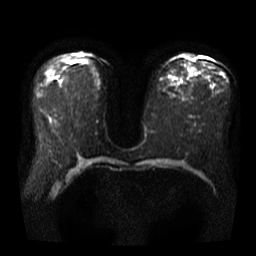
Breast MRI, one axial slice. Position 21 of 40 along the scan axis. Diffusion-weighted series; image 2 of 4 stored at this slice position (different b-values; order by instance number). 3 T. 256 × 256 image matrix. Female patient.
Structures marked on this image (expert manual segmentation):
- tumour on diffusion-weighted imaging: bounding box (x1, y1, x2, y2) in pixels: (187, 53, 192, 58)